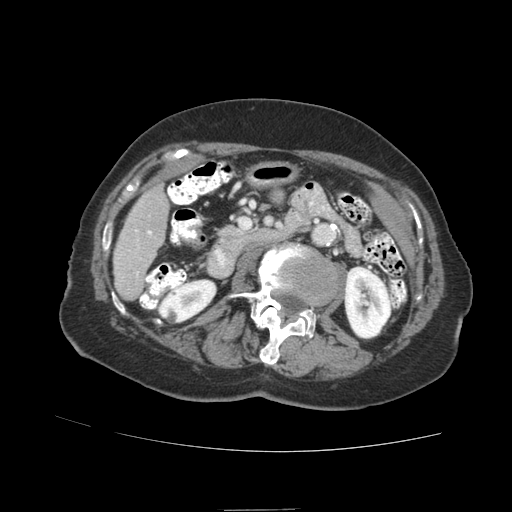
Contrast-enhanced abdominal CT (liver protocol), one axial slice; position 23 of 89 along the scan axis; reconstruction kernel STANDARD; soft-tissue window (W 400 / L 40 HU); 2.5 mm slice thickness; 512 × 512 image matrix, field of view 360 × 360 mm. Case-level facts recorded for this patient, not image findings: diagnosis: hepatocellular carcinoma (patient treated with transarterial chemoembolisation; whether this scan precedes or follows treatment is not stated here); TNM stage (as recorded): Stage-II; Child-Pugh class: A.
Outlined on this slice (semi-automatic segmentation, software-assisted and operator-edited):
- liver parenchyma outside the tumour (the mass and vessels are separate outlines, so this box may not span the whole liver): box from (x=112, y=184) to (x=168, y=300) px
- liver vessels: (x=136, y=230)–(x=152, y=275)